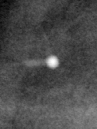
Crop from a digitized film mammogram around one marked abnormality; right breast; MLO view; BI-RADS breast density category 3 (scale 1–4).
Finding: calcifications, morphology round and regular / lucent centered; BI-RADS assessment category 2; subtlety rating 3 on a 1 (subtle) to 5 (obvious) scale; benign without callback (not worked up further).